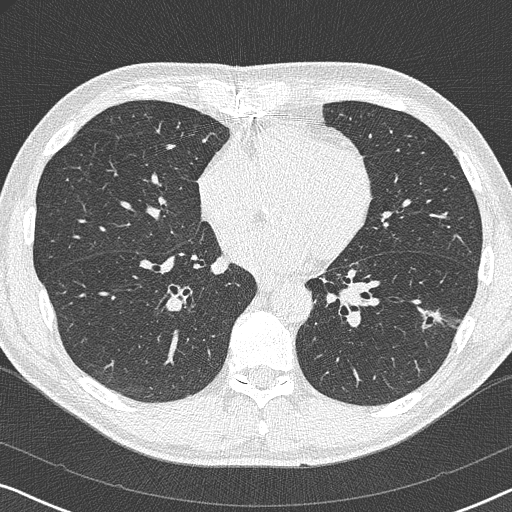
Axial slice from a low-dose chest CT screening exam. Baseline annual screen. Lung window (W 1500 / L -600 HU). 120 kVp. Slice 201 of 327 in the series. Male participant, aged 59 years at enrolment. Current smoker at enrolment.
• Lesion marked by an expert reader, box from (x=417, y=301) to (x=453, y=343) px.
• The screening reader recorded 2 non-calcified nodules or masses ≥4 mm on this exam (left lower lobe, right middle lobe); which of them this box marks is not recorded.
• Official screen result: positive, change unspecified: nodule(s) >= 4 mm or enlarging nodule(s), mass(es), or other non-specific abnormalities suspicious for lung cancer.
• Later outcome: lung cancer diagnosed 821 days after this screen (after the third annual screen) — adenocarcinoma, NOS, left lower lobe, poorly differentiated (G3), stage IA (AJCC 6th edition), 20 mm at pathology.